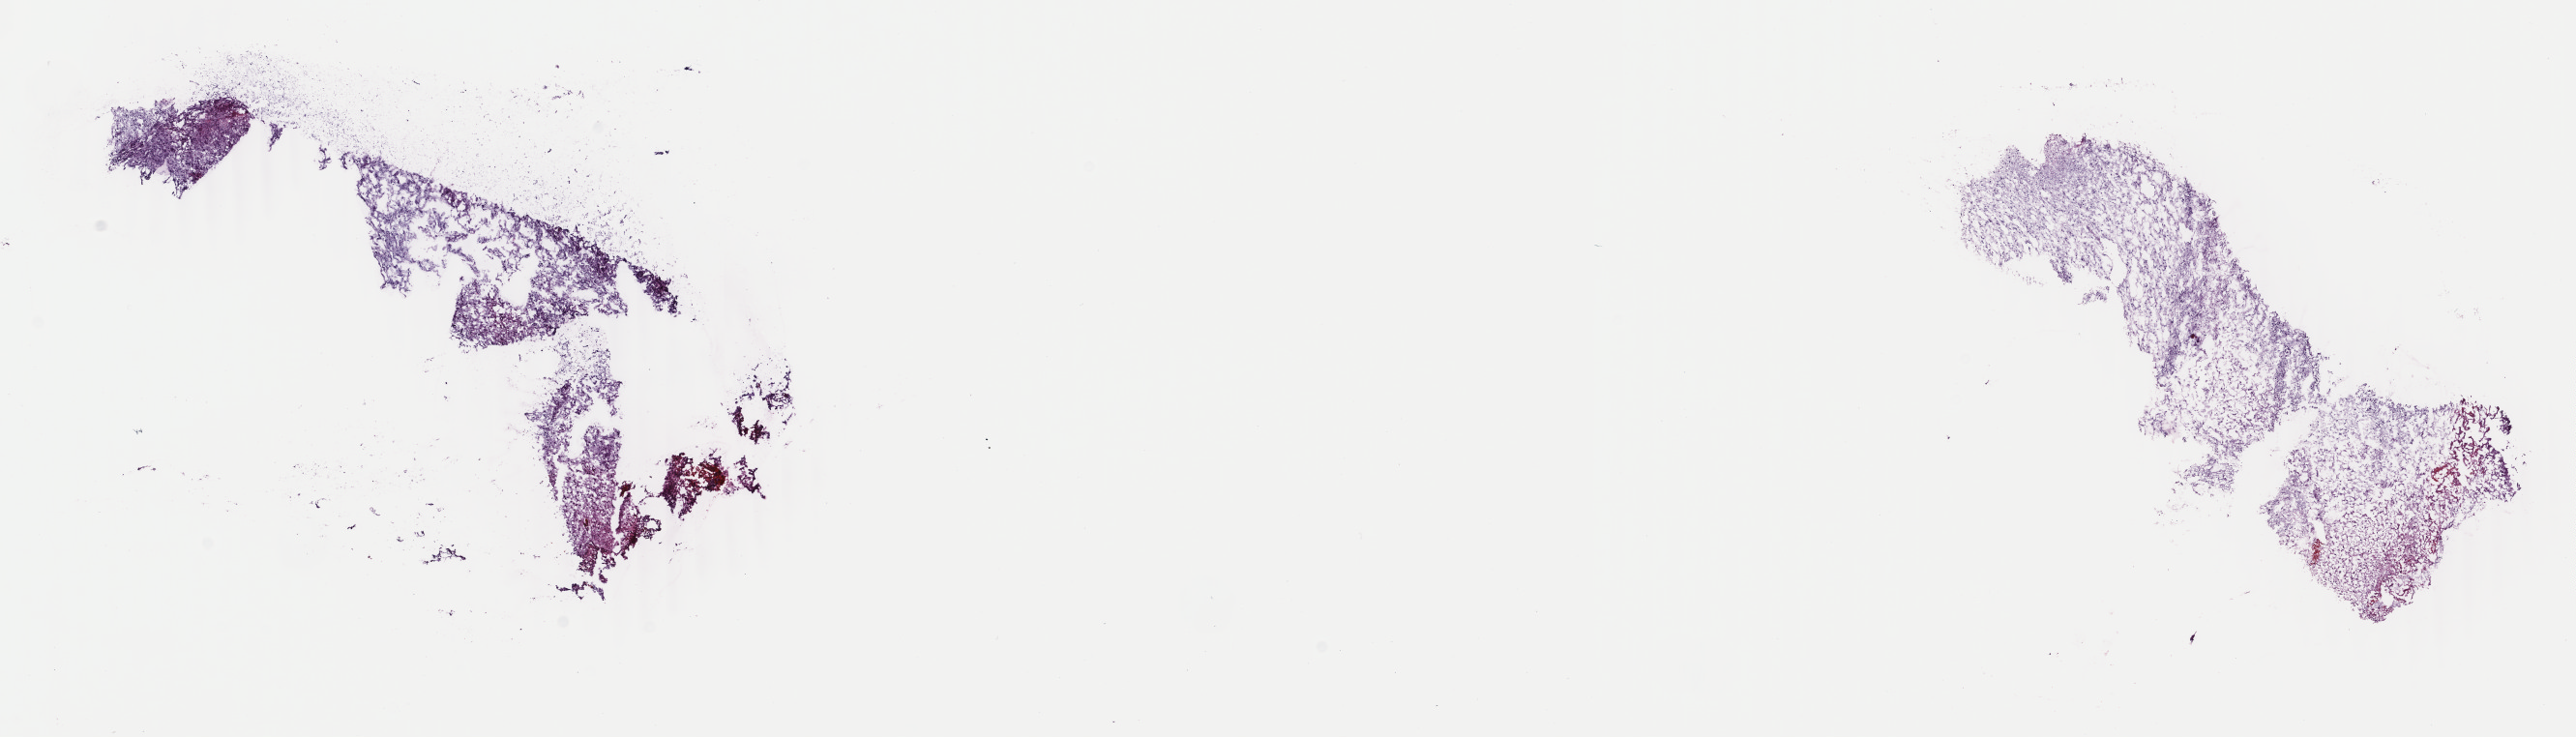
H&E-stained whole-slide image — shown as a low-resolution overview of the whole scanned area (about 21.2 x 6.1 mm, acquisition: 40x scan). Frozen section from the top of the tissue portion. Sample: primary tumour, brain. Male, age 31 years at initial diagnosis. Histologic grade: G3 (poorly differentiated). Composition of this section per pathologist review: tumour cells 40%, tumour nuclei 70%, normal cells 10%, stromal cells 50%, necrosis 0%. Infiltration values recorded for this section: lymphocyte infiltration 0%, monocyte infiltration 0%, neutrophil infiltration 0%.
* laterality: right
* pathologic diagnosis: Astrocytoma, anaplastic